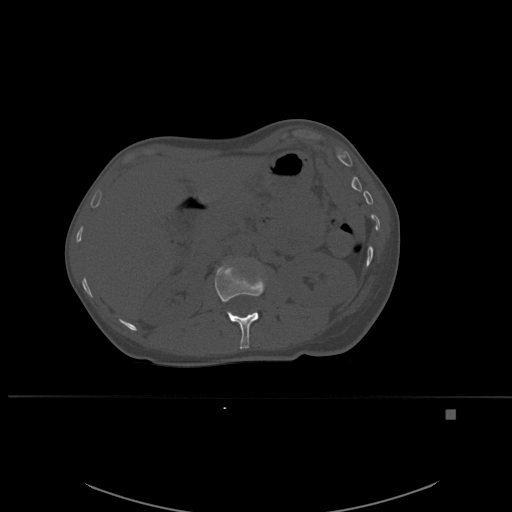
CT including the spine, one axial slice; slice 254 of 537 in the series (ordered by position); bone window (W 1800 / L 400 HU); 512 × 512 image matrix, field of view 440 × 440 mm. Female patient, age 45 years. Case-level facts recorded for this patient, not image findings: primary cancer: lung.
Outlined on this slice (semi-automatic segmentation, software-assisted and operator-edited):
- L1 vertebra: bounding box [x1, y1, x2, y2] px = [215, 261, 266, 349]